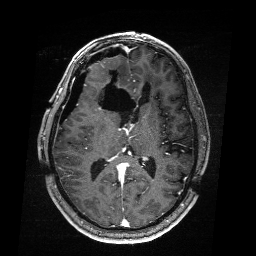
Brain MRI from a brain-tumour surgery series, one axial slice. Position 98 of 176 along the scan axis. T1-weighted post-contrast. 1 mm slice thickness. 256 × 256 image matrix, field of view 256 × 256 mm. From the clinical record (not read from this slice): histopathology: Astrocytoma; WHO grade: 4.
Structures marked on this image (expert manual segmentation):
- residual tumour: bounding box (x1, y1, x2, y2) in pixels: (101, 82, 110, 136)